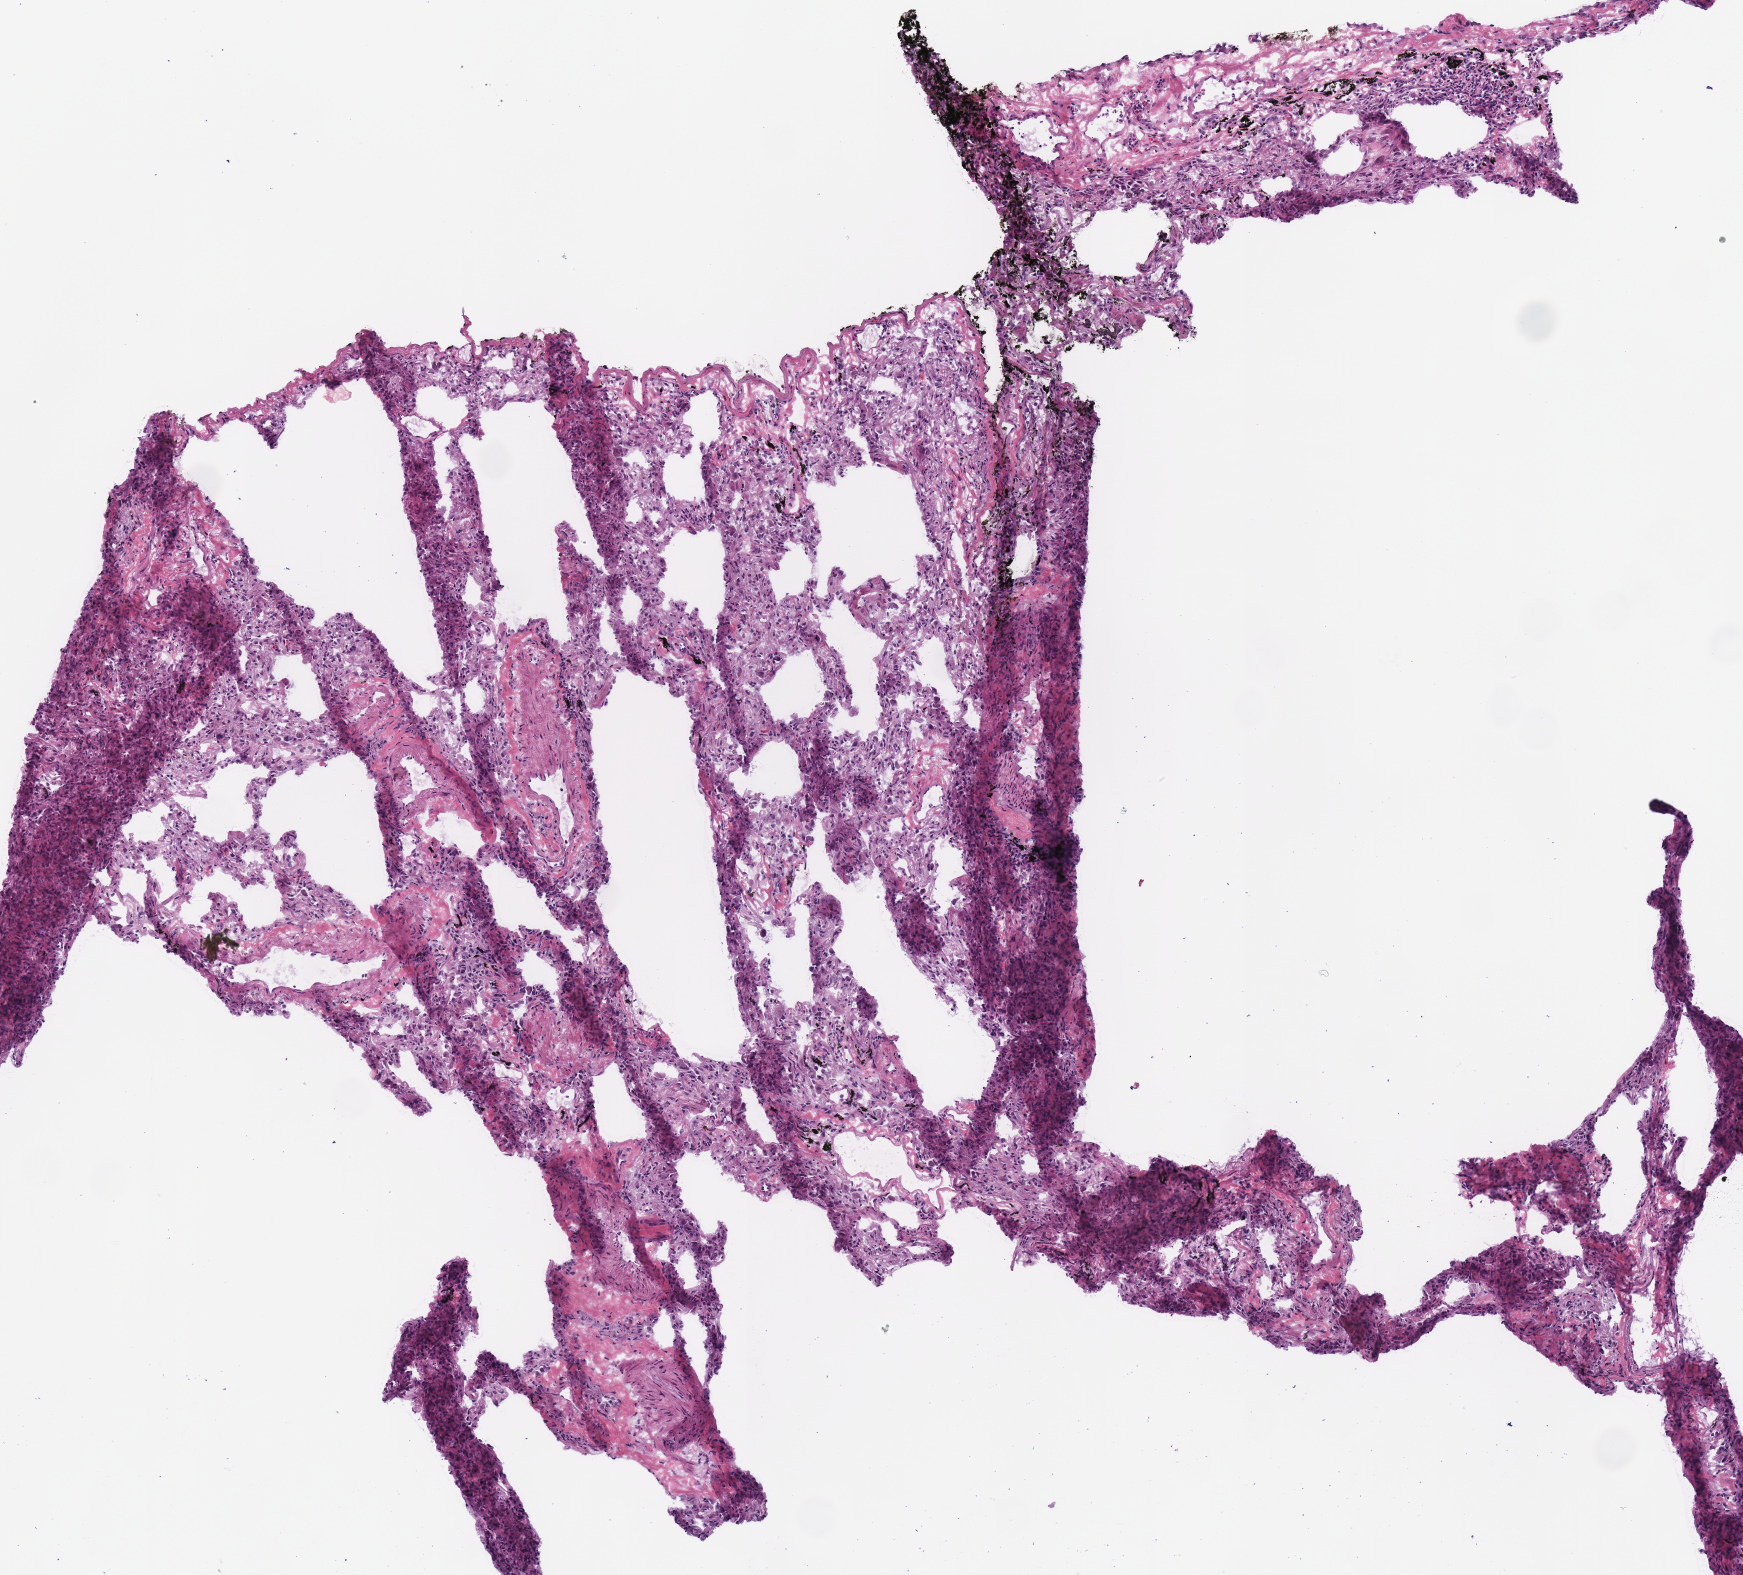
H&E whole-slide image, shown as a low-resolution overview of the whole scanned area (about 3.4 x 3.1 mm, acquisition: 40x scan), frozen section from the top of the tissue portion, solid tissue normal (non-tumour tissue) sample from the lung. Patient: male, age at initial diagnosis 58 years.
This section: solid tissue normal (non-tumour) sample from the same patient. Patient diagnosis: Adenocarcinoma, NOS (lower lobe, lung).